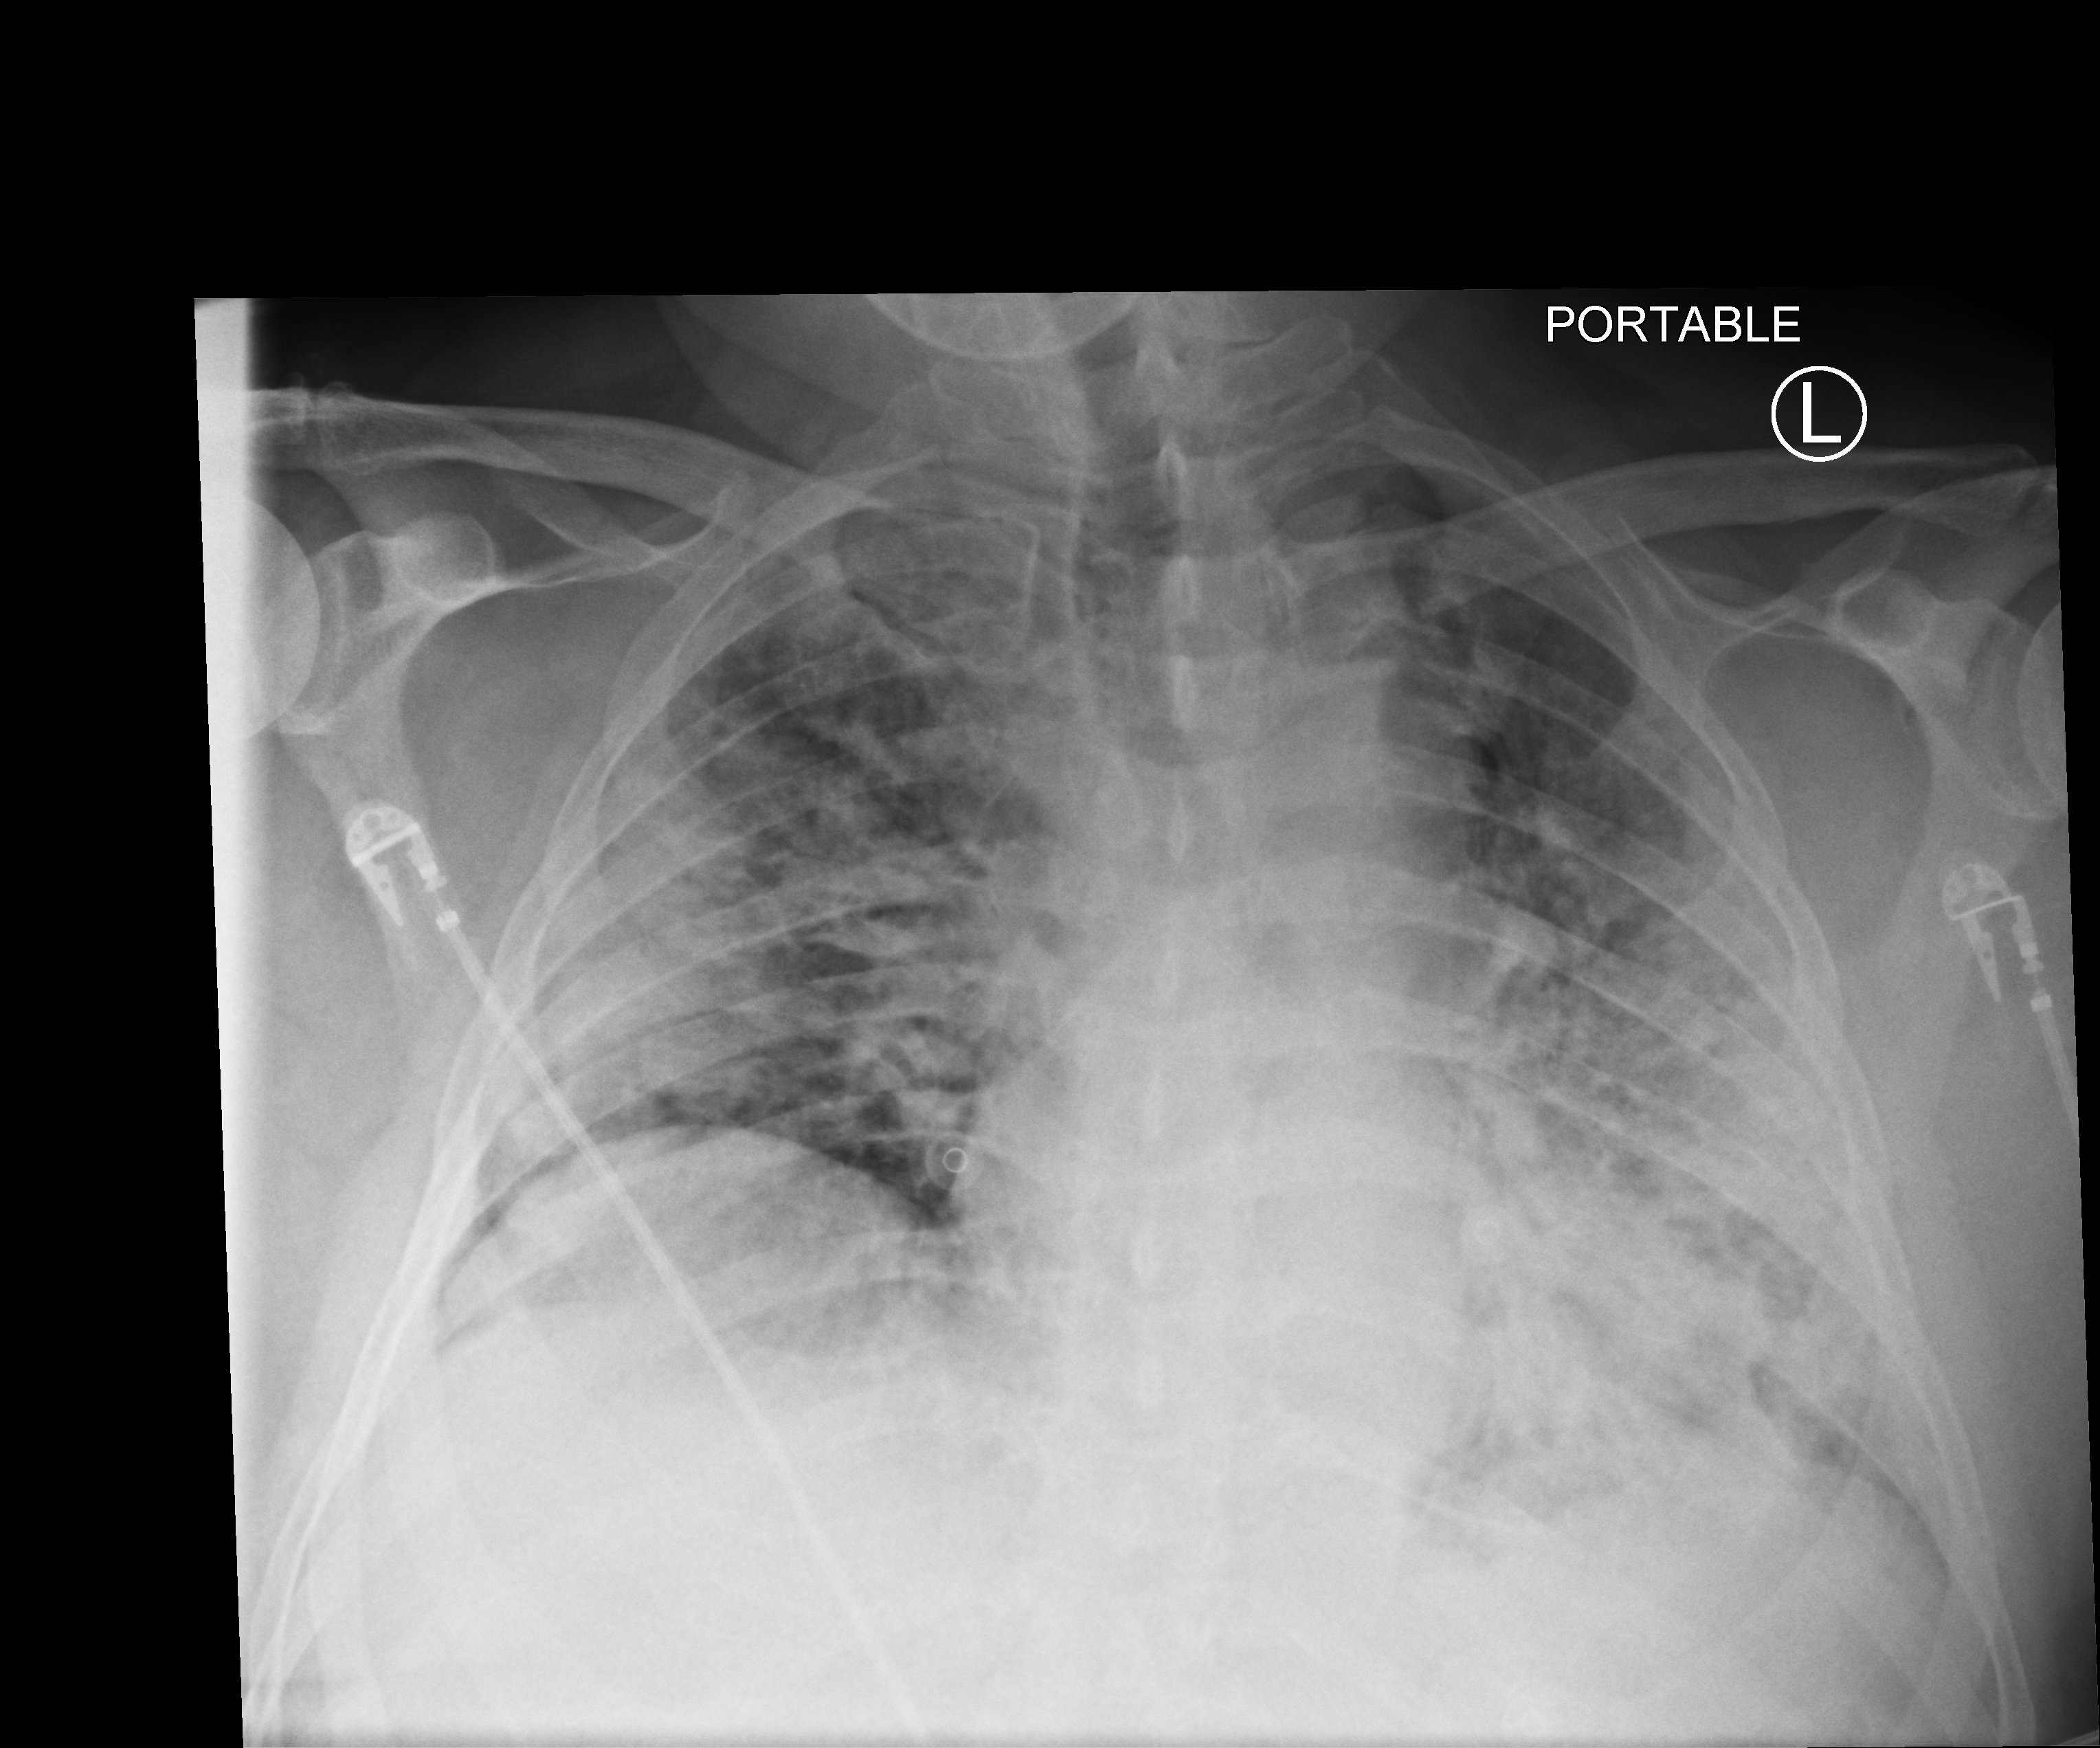
Bedside chest radiograph (computed radiography), anteroposterior (AP) projection. Male patient hospitalised with COVID-19, age 60–74 years.
From the hospital-stay record, not from the radiograph (when in the stay this image was taken is not recorded):
- mechanically ventilated during this hospital stay: yes
- admitted to intensive care during this hospital stay: yes
- other chronic lung disease (admission record): no